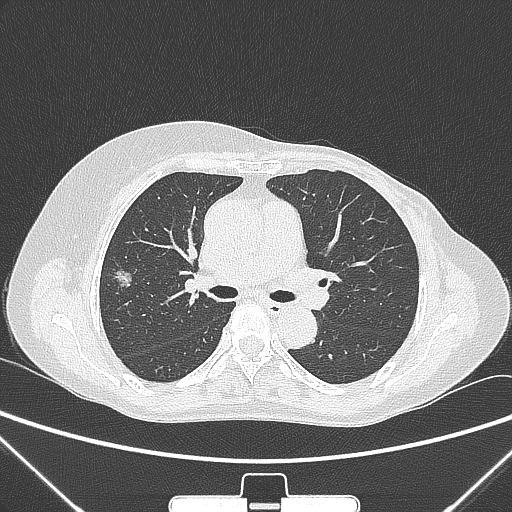
Chest CT, one axial slice. Position 154 of 265 along the scan axis. 120 kVp. Lung window (W 1500 / L -600 HU). 512 × 512 image matrix. Female patient, age 64 years. From the clinical record (not read from this slice): clinical TNM (as recorded): T1c N0 M0; histopathological grade: G1-2.
Annotated regions visible in this slice (rectangle marked by the reading radiologist):
- lung tumour (recorded histology: adenocarcinoma): bounding box (x1, y1, x2, y2) in pixels: (110, 264, 140, 297)